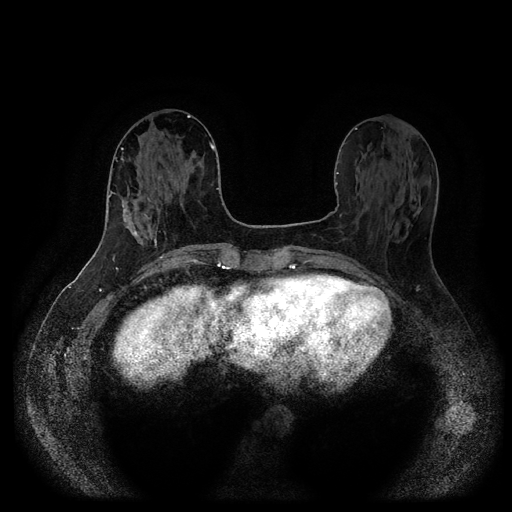
Breast MRI (dynamic contrast-enhanced, multi-phase), one axial slice; slice 41 of 116 in the series (ordered by position); dynamic contrast-enhanced series, time point 2 of 5 at this slice position (early post-contrast); 1.5 T; TE 2.6 ms, TR 5.3 ms; 2 mm slice thickness; 512 × 512 image matrix, field of view 360 × 360 mm. Patient: female, 58 years.
Annotated regions visible in this slice (semi-automatically segmented with operator editing):
- breast lesion (labelled 'tumour' in the annotation; benign lesions carry a separate 'benign' label): box from (x=132, y=226) to (x=141, y=240) px